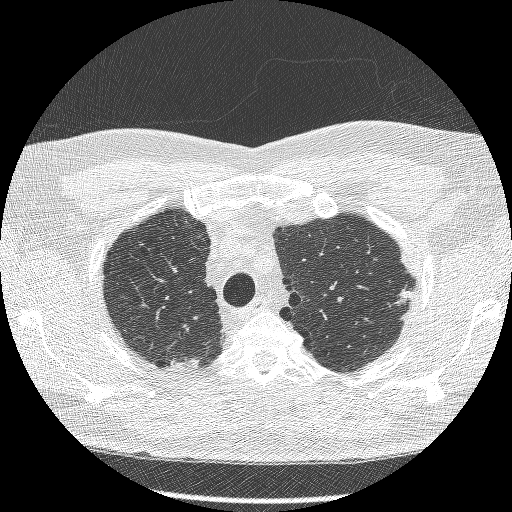
Axial slice from a low-dose chest CT screening exam, second screening round (one year after baseline), lung window (W 1500 / L -600 HU), slice 225 of 269 in the series, 512 × 512 image matrix. Male participant, aged 66 years at enrolment. Current smoker at enrolment.
Lesion marked by an expert reader, bounding box <382,264,427,317> (left, top, right, bottom; pixels). Screening reader's record for this exam (one nodule recorded; not confirmed to be the boxed lesion): non-calcified nodule or mass ≥4 mm, right lower lobe, 40 × 19 mm, spiculated (stellate) margins, soft tissue attenuation, pre-existing on the prior screen: yes; interval growth: no. Note: the box lies in the patient's left hemithorax on this image, whereas the reader's record names the right lung; they may be different findings. Participant outcome: lung cancer diagnosed 554 days after this screen (after the third annual screen) — adenocarcinoma, NOS, left upper lobe, poorly differentiated (G3), stage IB (AJCC 6th edition), 16 mm at pathology.